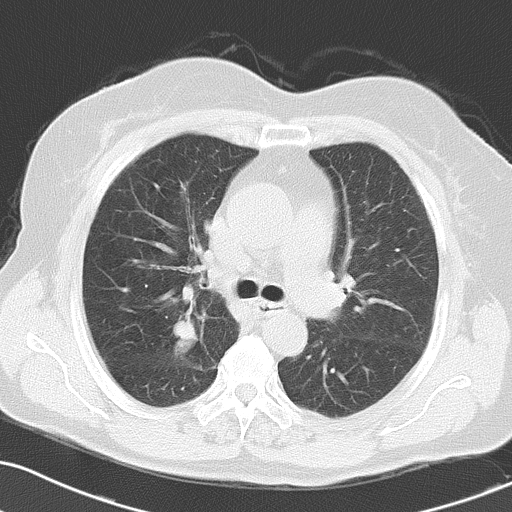
Chest CT, one axial slice. Position 37 of 55 along the scan axis. 120 kVp. Lung window (W 1500 / L -600 HU). 5 mm slice thickness. 512 × 512 image matrix, field of view 323 × 323 mm. Patient: female, 70 years. From the clinical record (not read from this slice): clinical TNM (as recorded): T1c N3 M0.
Structures marked on this image (rectangle marked by the reading radiologist):
- lung tumour (recorded histology: small cell carcinoma): bounding box (x1, y1, x2, y2) in pixels: (171, 311, 200, 365)